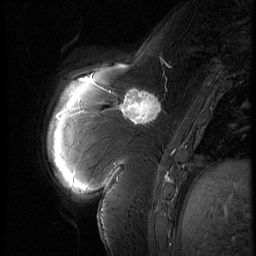
Breast MRI (dynamic contrast-enhanced), one sagittal slice; position 17 of 60 along the scan axis; 3 images stored at this slice position (order not interpretable as contrast timing); 1.5 T; TE 4.2 ms, TR 9 ms; 2.5 mm slice thickness; 256 × 256 image matrix, field of view 180 × 180 mm. Female patient, age 57 years. From the clinical record (not read from this slice): setting: breast cancer imaged before/during neoadjuvant chemotherapy; receptor status: triple-negative.
Annotated regions visible in this slice (semi-automatic segmentation, software-assisted and operator-edited):
- analysis volume of interest (the breast-tissue region the enhancement analysis was run in; not a lesion): box from (x=114, y=83) to (x=170, y=131) px
- tumour enhancement mask (voxels above the 140 % enhancement threshold inside the analysis volume of interest): (x=121, y=91)–(x=160, y=125)